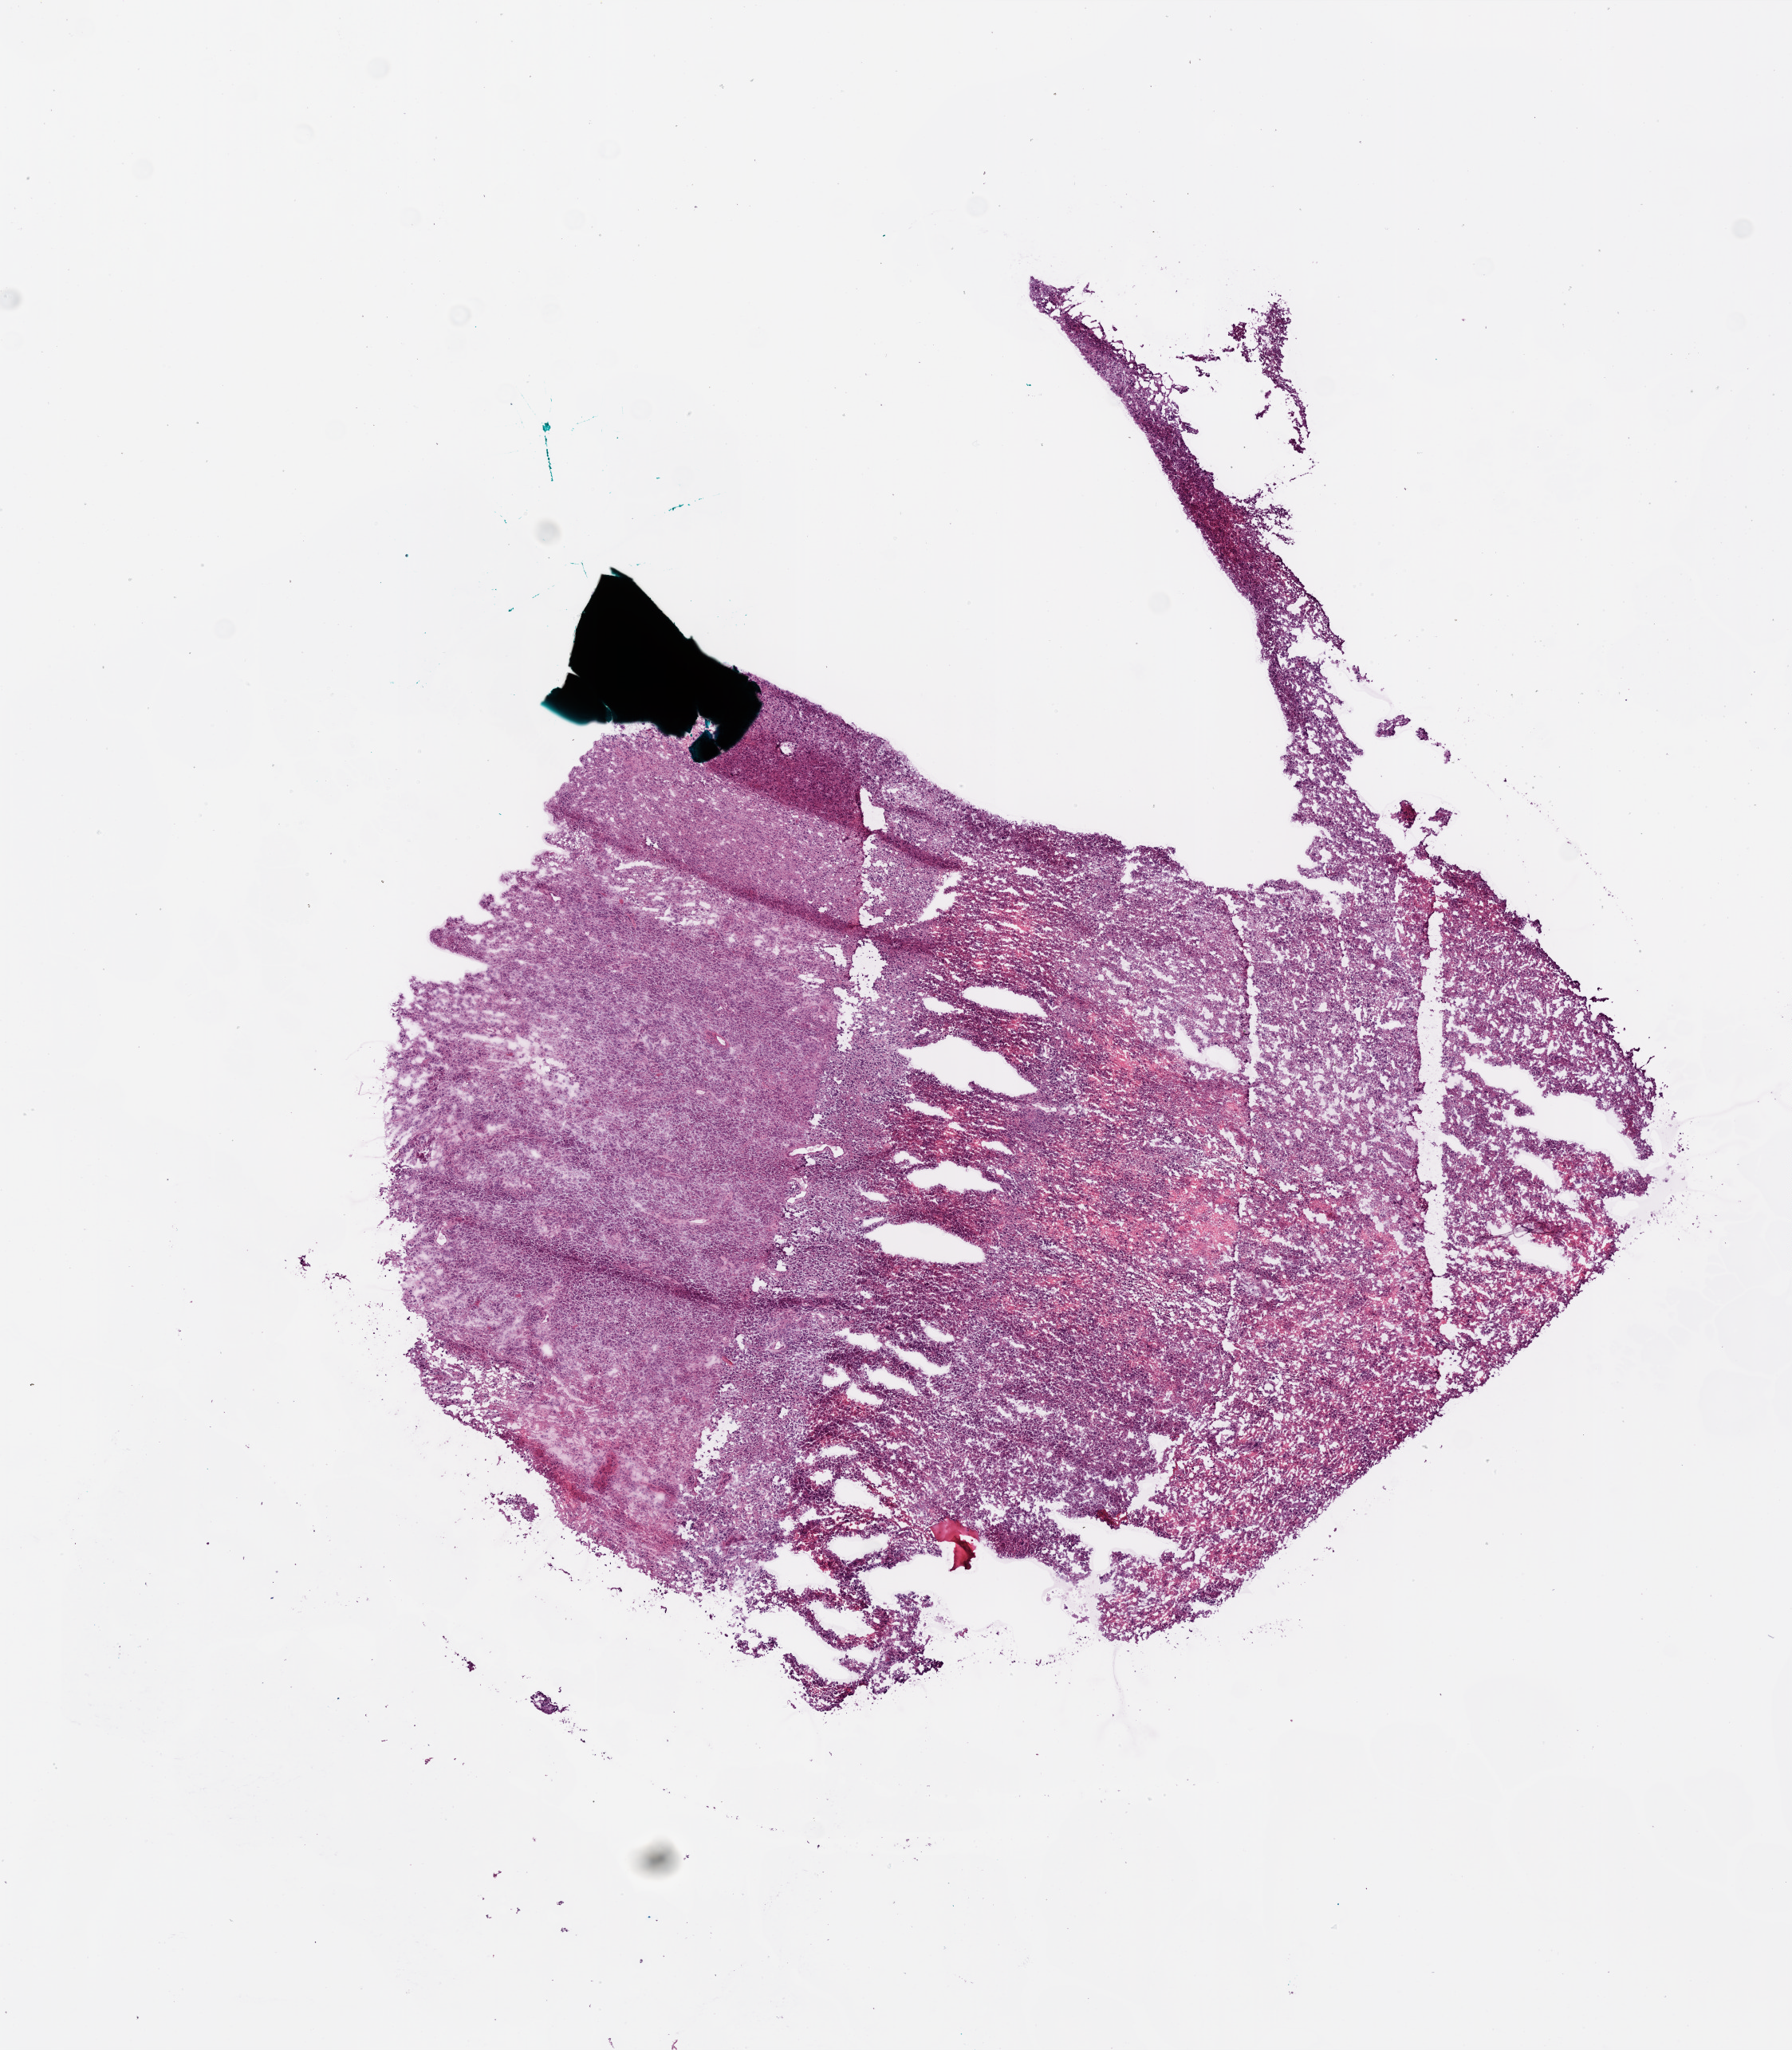
Whole-slide histology image, Hematoxylin and eosin (H&E) stained, shown as a low-resolution overview of the whole scanned area (about 9.0 x 10.3 mm). Frozen section from the bottom of the tissue portion. Primary tumour sample from the brain. Patient: female, age at initial diagnosis 83 years.
Pathologic diagnosis: Glioblastoma.